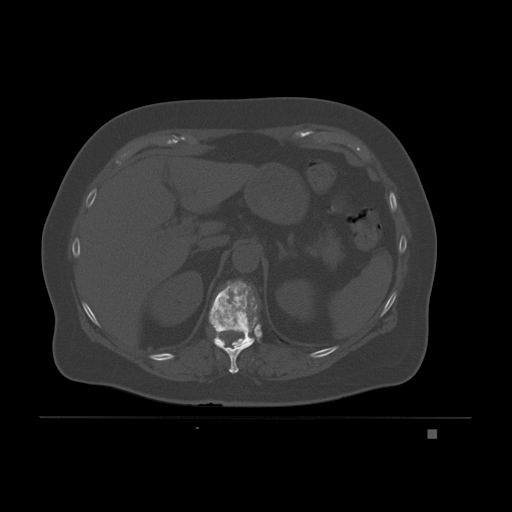
CT including the spine, one axial slice; position 94 of 221 along the scan axis; bone window (W 1800 / L 400 HU); 512 × 512 image matrix. Patient: female, 63 years. Case-level facts recorded for this patient, not image findings: primary cancer: breast.
Structures marked on this image (semi-automatically segmented with operator editing):
- T10 vertebra: bounding box [x1, y1, x2, y2] px = [214, 341, 252, 374]
- T11 vertebra: [209, 281, 258, 346]